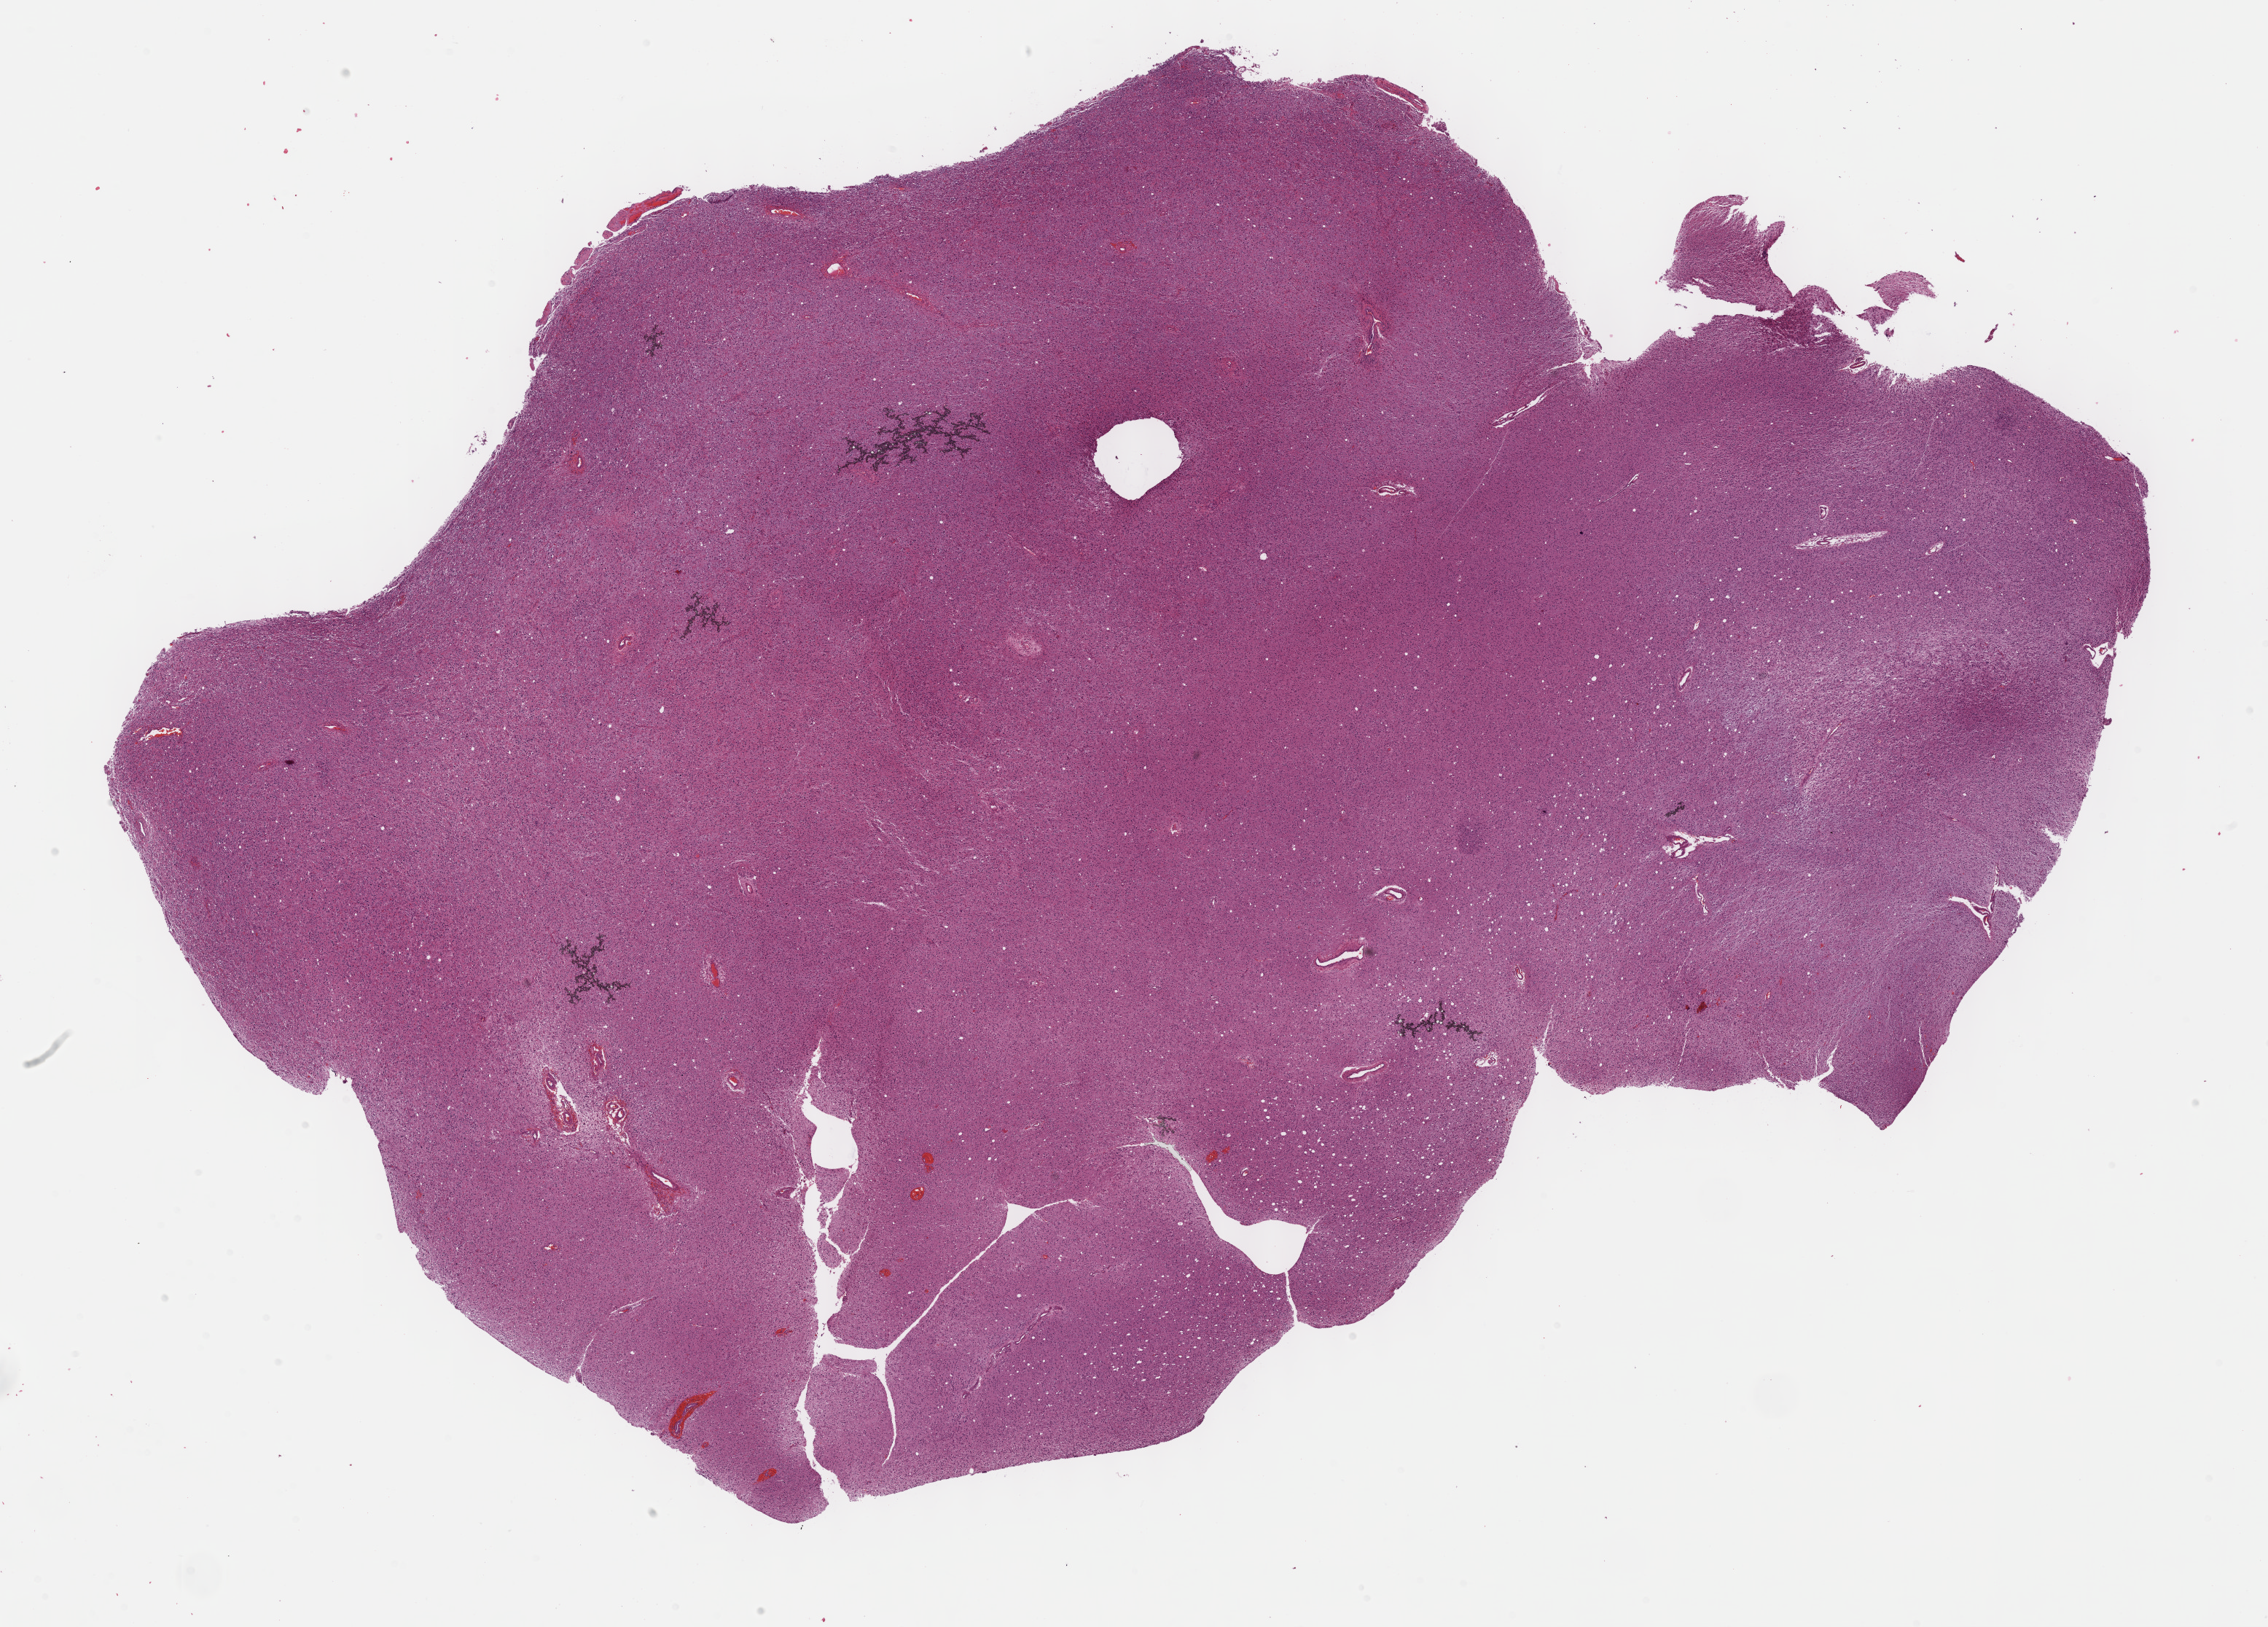
Digitized H&E tissue section (whole slide), low-resolution overview of the scanned area, about 25.2 x 18.1 mm (acquisition: 40x scan), FFPE section, sample: primary tumour, brain. Patient: male, age at initial diagnosis 34 years.
Pathologic diagnosis: Mixed glioma (cerebrum).